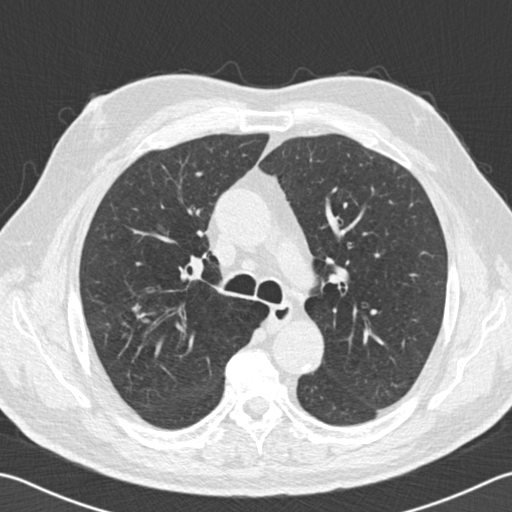
Low-dose screening chest CT, one axial slice. Reconstruction kernel B30f. 120 kVp. Lung window (W 1500 / L -600 HU). 2 mm slice thickness. 512 × 512 image matrix, field of view 346 × 346 mm.
Outlined on this slice (outlined manually by an expert reader):
- lesion 1 (tumor, upper lobe of right lung): bounding box [x1, y1, x2, y2] px = [133, 306, 145, 318]